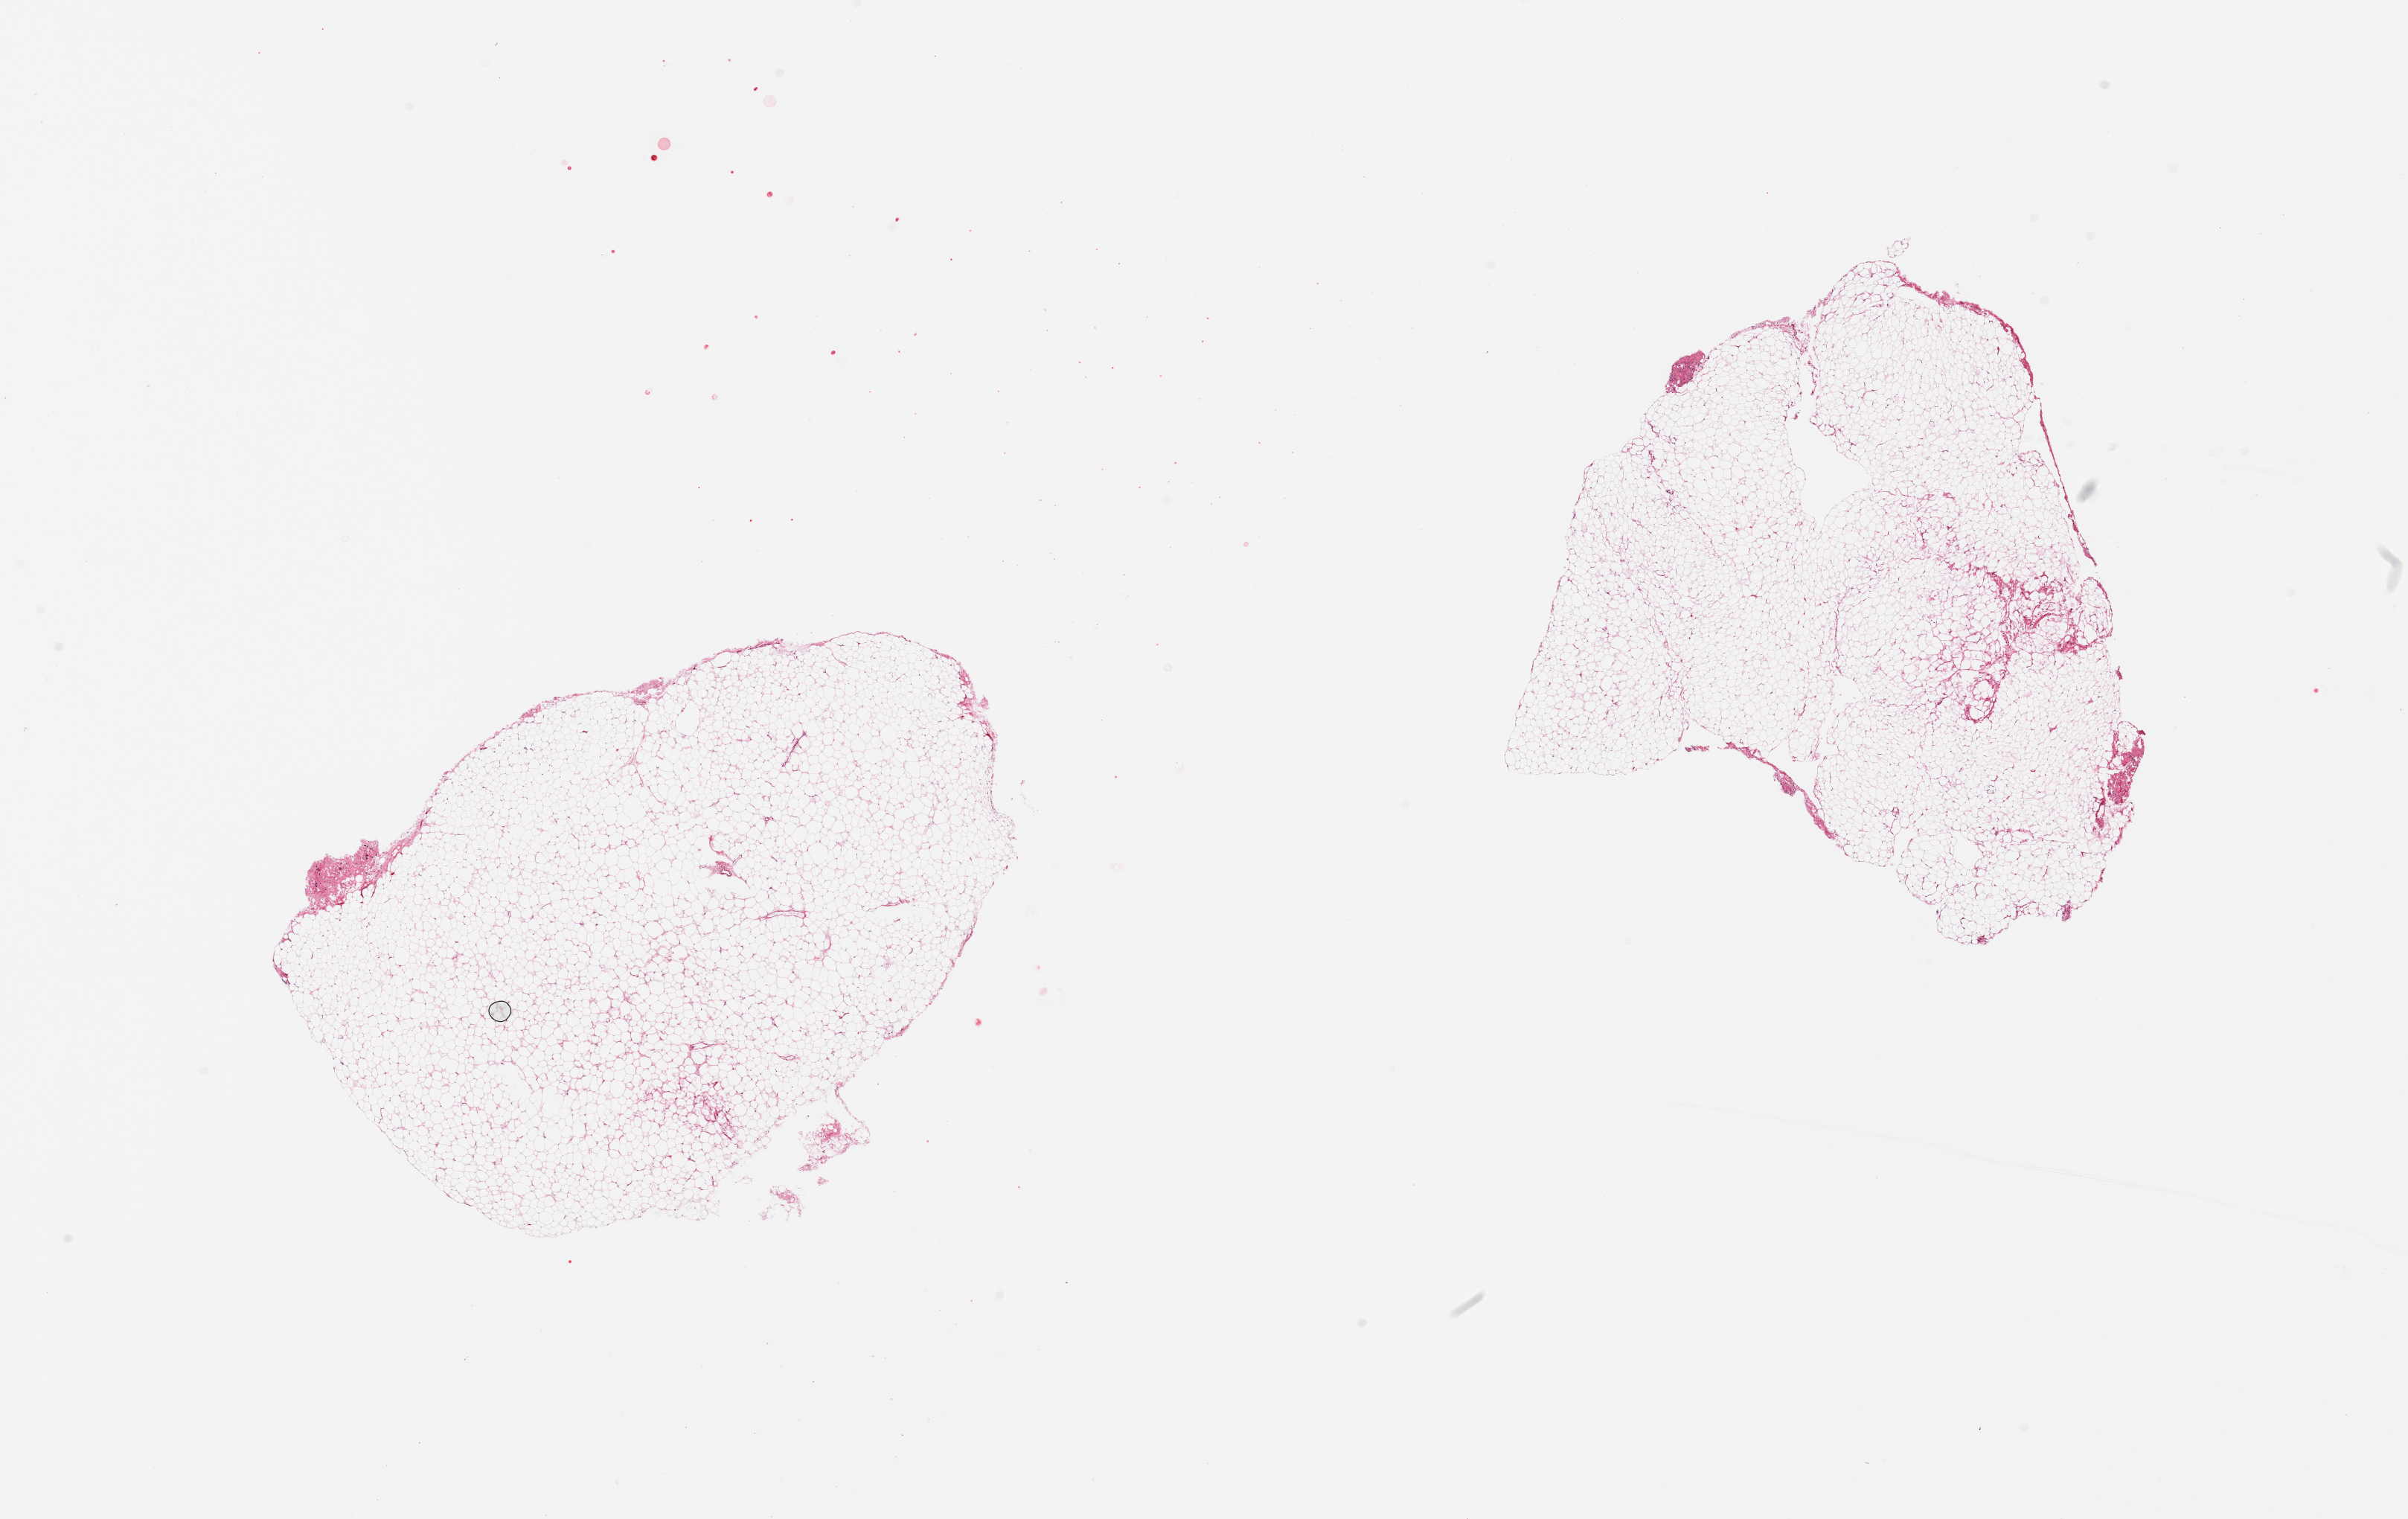
Whole-slide image, hematoxylin and eosin (H&E) stain, whole scanned area (about 25.6 x 16.1 mm, acquisition: 20x scan) shown as a low-resolution overview, PAXgene-fixed, paraffin-embedded tissue, section of omentum (target tissue), tissue donor sample. Donor: female.
Pathologist's review note for this sample: 2 pieces; 1% fibrous content.